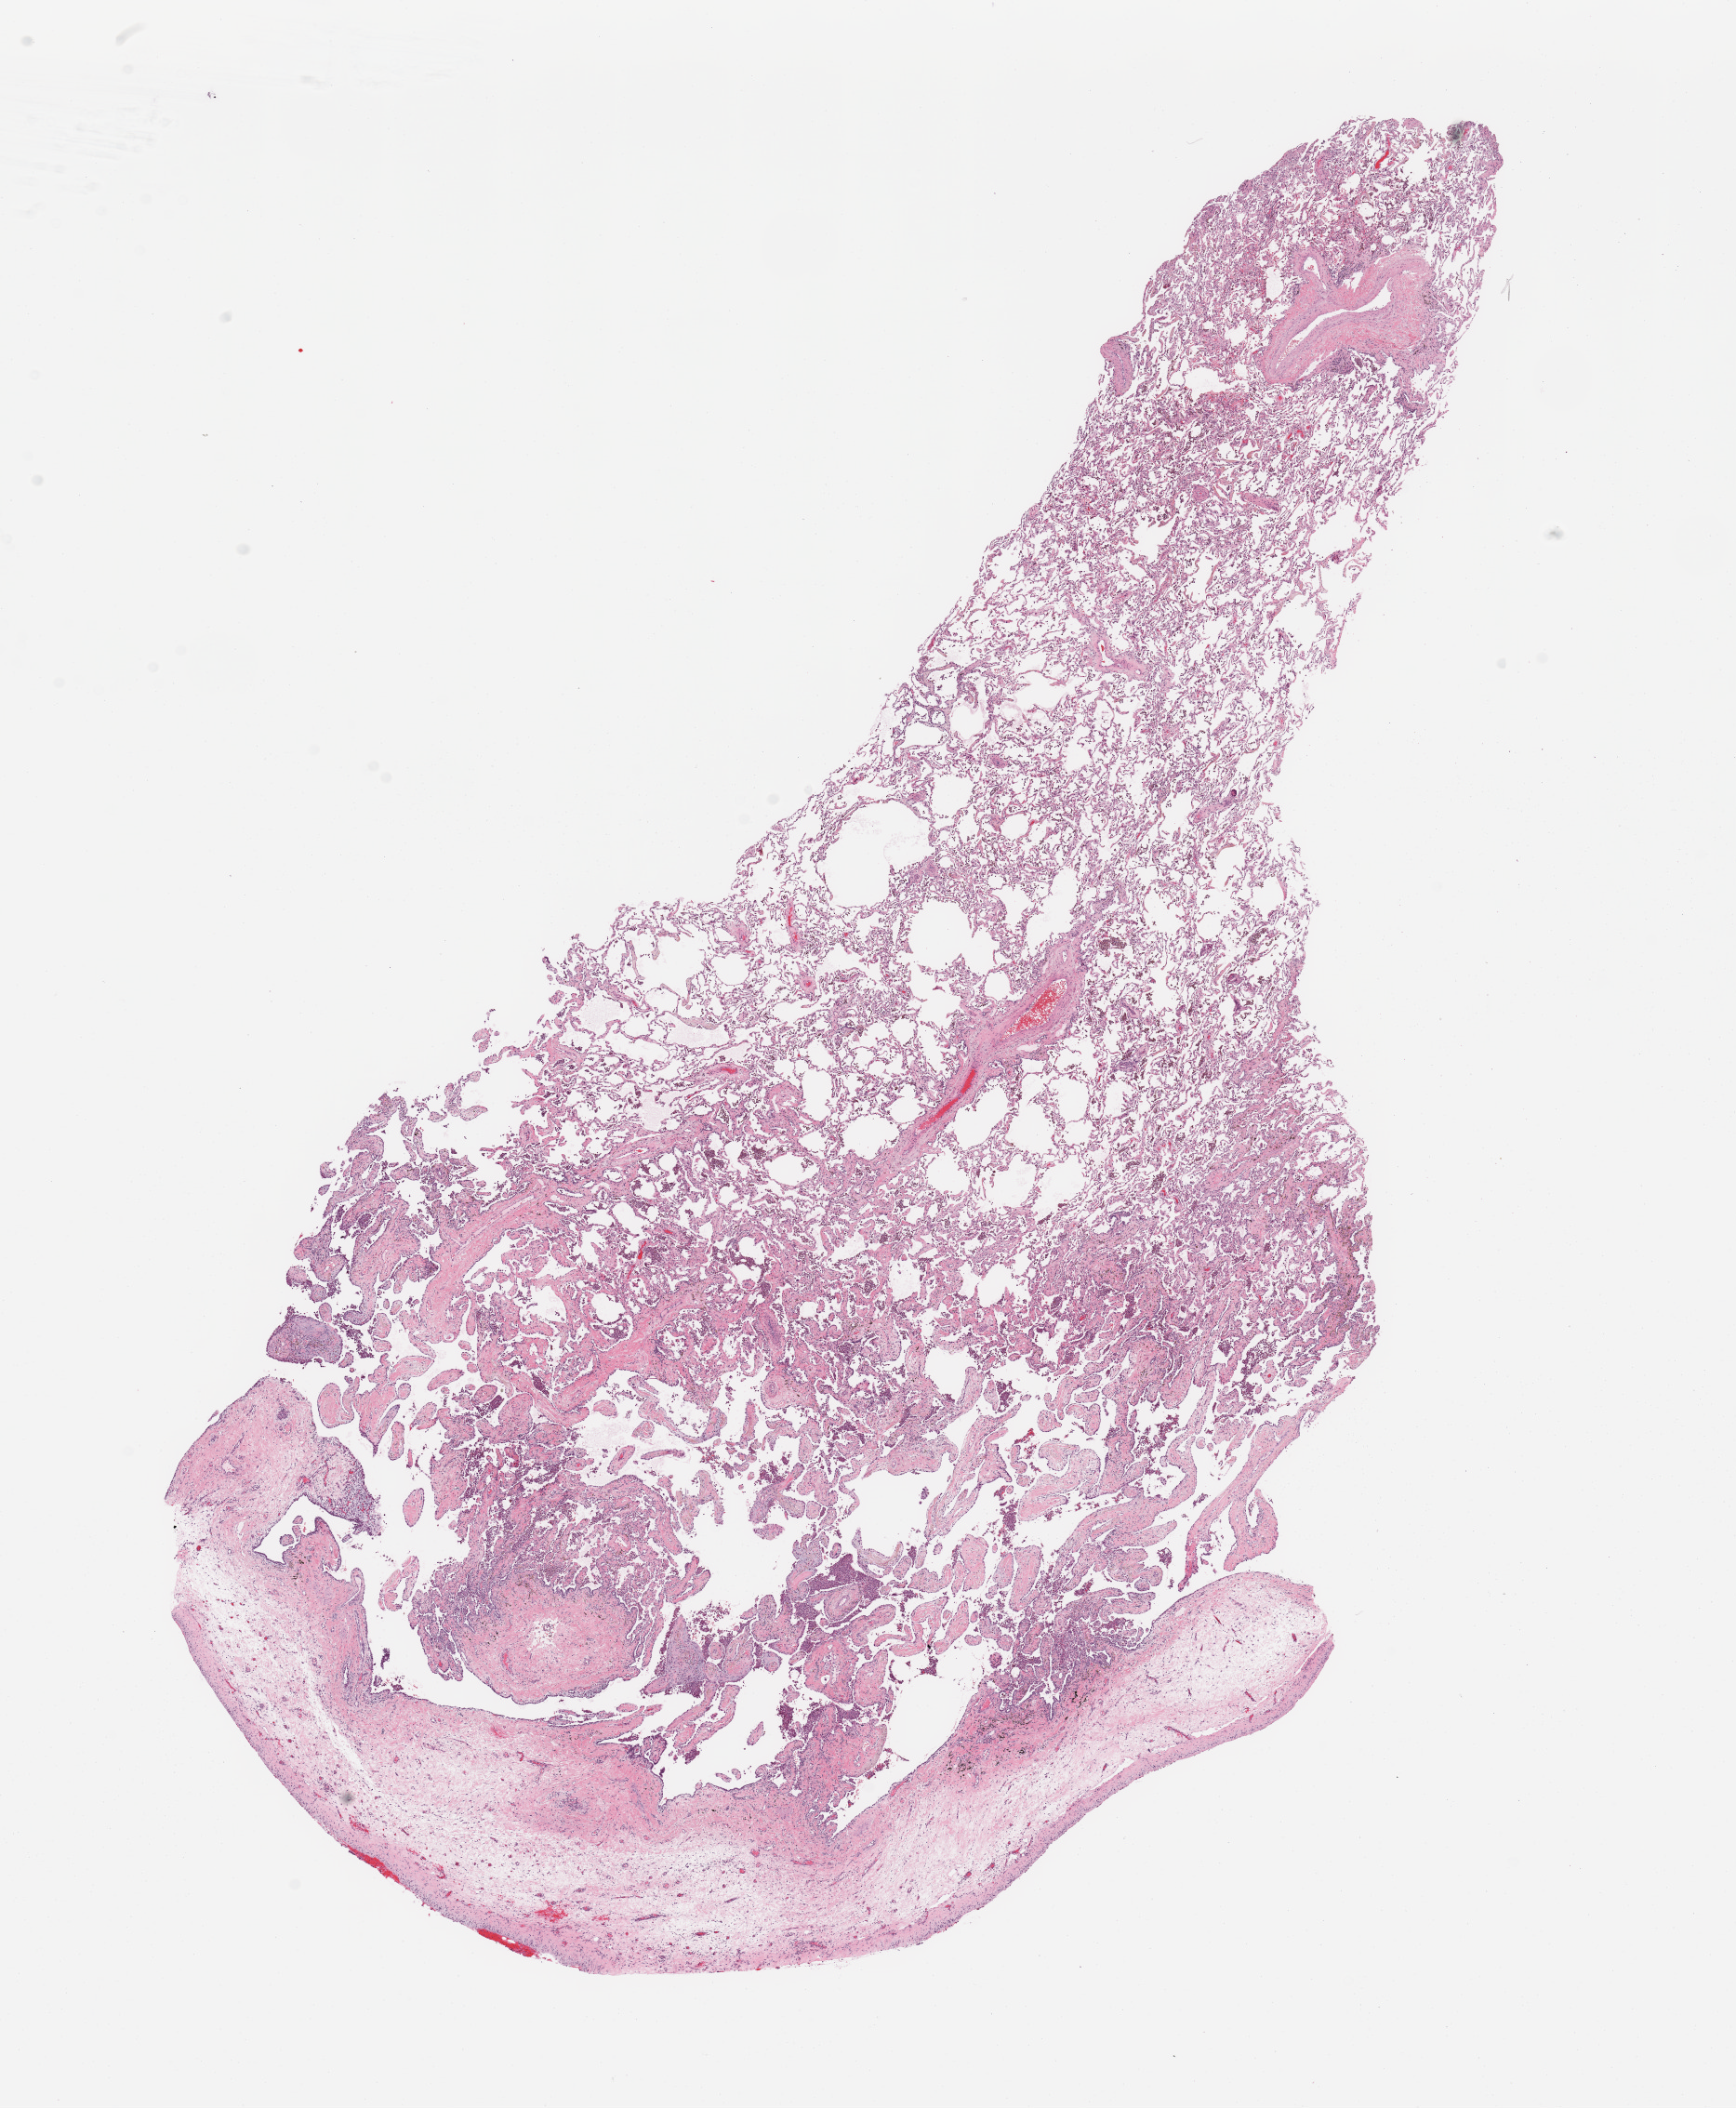
Hematoxylin and eosin (H&E) stained whole-slide image, low-resolution overview of the scanned area, about 14.8 x 17.9 mm (from a 20x scan); normal (non-tumour) tissue sample, sampled site: lung. Patient: male, age 58 years.
This section: normal (non-tumour) tissue from the same patient. Patient diagnosis: Adenocarcinoma, NOS.